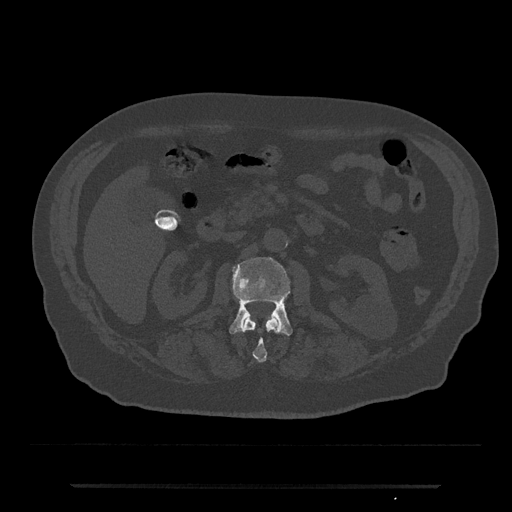
CT including the spine, one axial slice; position 496 of 797 along the scan axis; reconstruction kernel Br40s/3; 120 kVp; bone window (W 1800 / L 400 HU); 0.5 mm slice thickness; 512 × 512 image matrix. Male patient, age 80 years. Case-level facts recorded for this patient, not image findings: primary cancer: prostate; vertebrae with lytic lesions (as recorded): L1, T11.
Structures marked on this image (semi-automatically segmented with operator editing):
- L1 vertebra: box from (x=243, y=317) to (x=281, y=362) px
- L2 vertebra: (x=229, y=257)–(x=293, y=335)